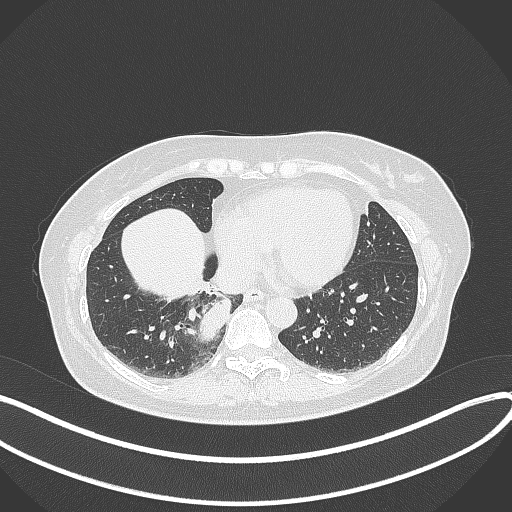
Chest CT, one axial slice. Position 110 of 331 along the scan axis. Reconstruction kernel B70f. 120 kVp. Lung window (W 1500 / L -600 HU). 1 mm slice thickness. 512 × 512 image matrix. Patient: female, 54 years. Case-level facts recorded for this patient, not image findings: clinical TNM (as recorded): T4 N0 M0.
Structures marked on this image (rectangle marked by the reading radiologist):
- lung tumour (recorded histology: adenocarcinoma): bounding box <194,297,230,345> (left, top, right, bottom; pixels)